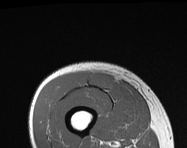
MRI of an extremity soft-tissue mass, one axial slice; slice 34 of 114 in the series (ordered by position); MR volume resampled by the dataset authors to the PET/CT grid (not the native acquisition matrix); 3.27 mm slice thickness; 187 × 148 image matrix, field of view 183 × 145 mm. Male patient. Case-level facts recorded for this patient, not image findings: histological type: pleiomorphic leiomyosarcoma; grade: intermediate; site of the primary tumour: right thigh.
Structures marked on this image (expert contour drawn on MRI and transferred to this co-registered scan by the dataset authors):
- gross tumour volume including surrounding oedema: box from (x=88, y=72) to (x=113, y=89) px